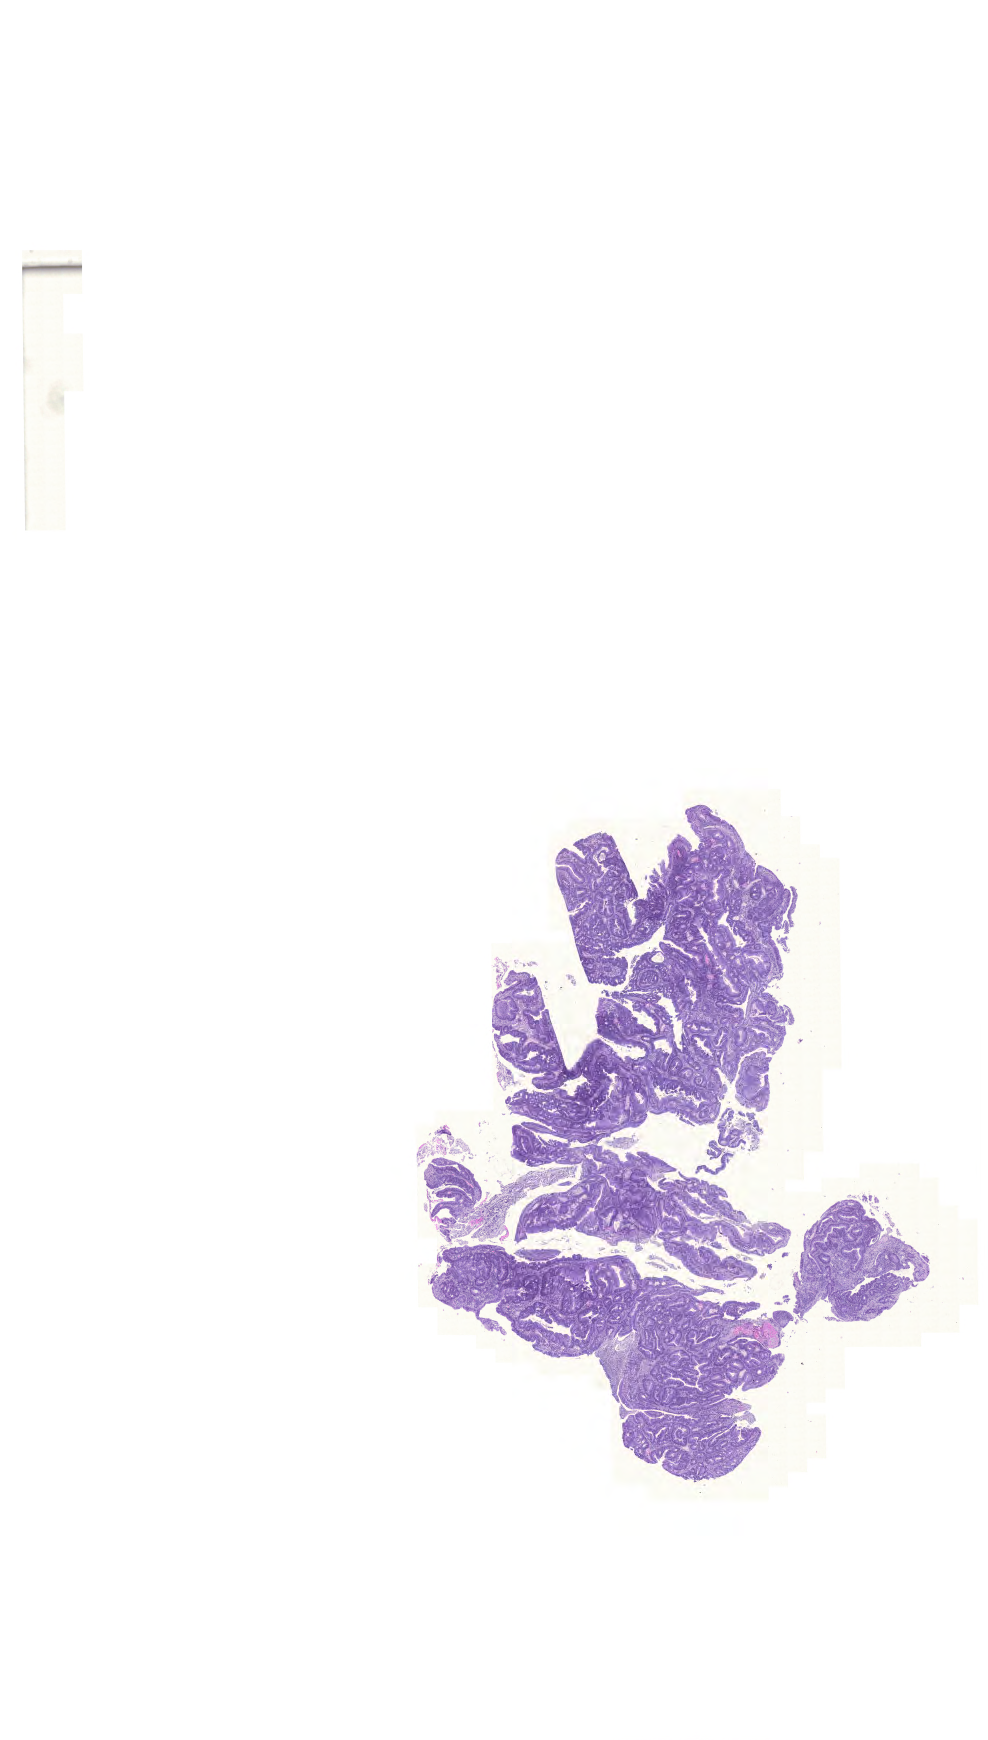
Digitized H&E tissue section (whole slide) — whole scanned area (about 14.7 x 25.9 mm, from a 20x scan) shown as a low-resolution overview; formalin-fixed paraffin-embedded (FFPE) diagnostic section; sample: primary tumour, colon. Male patient; age at initial diagnosis 84 years.
Lymph nodes positive (case pathology): 5 of 19 examined. AJCC pathologic stage: IV (6th edition). Histologic diagnosis: Adenocarcinoma, NOS.